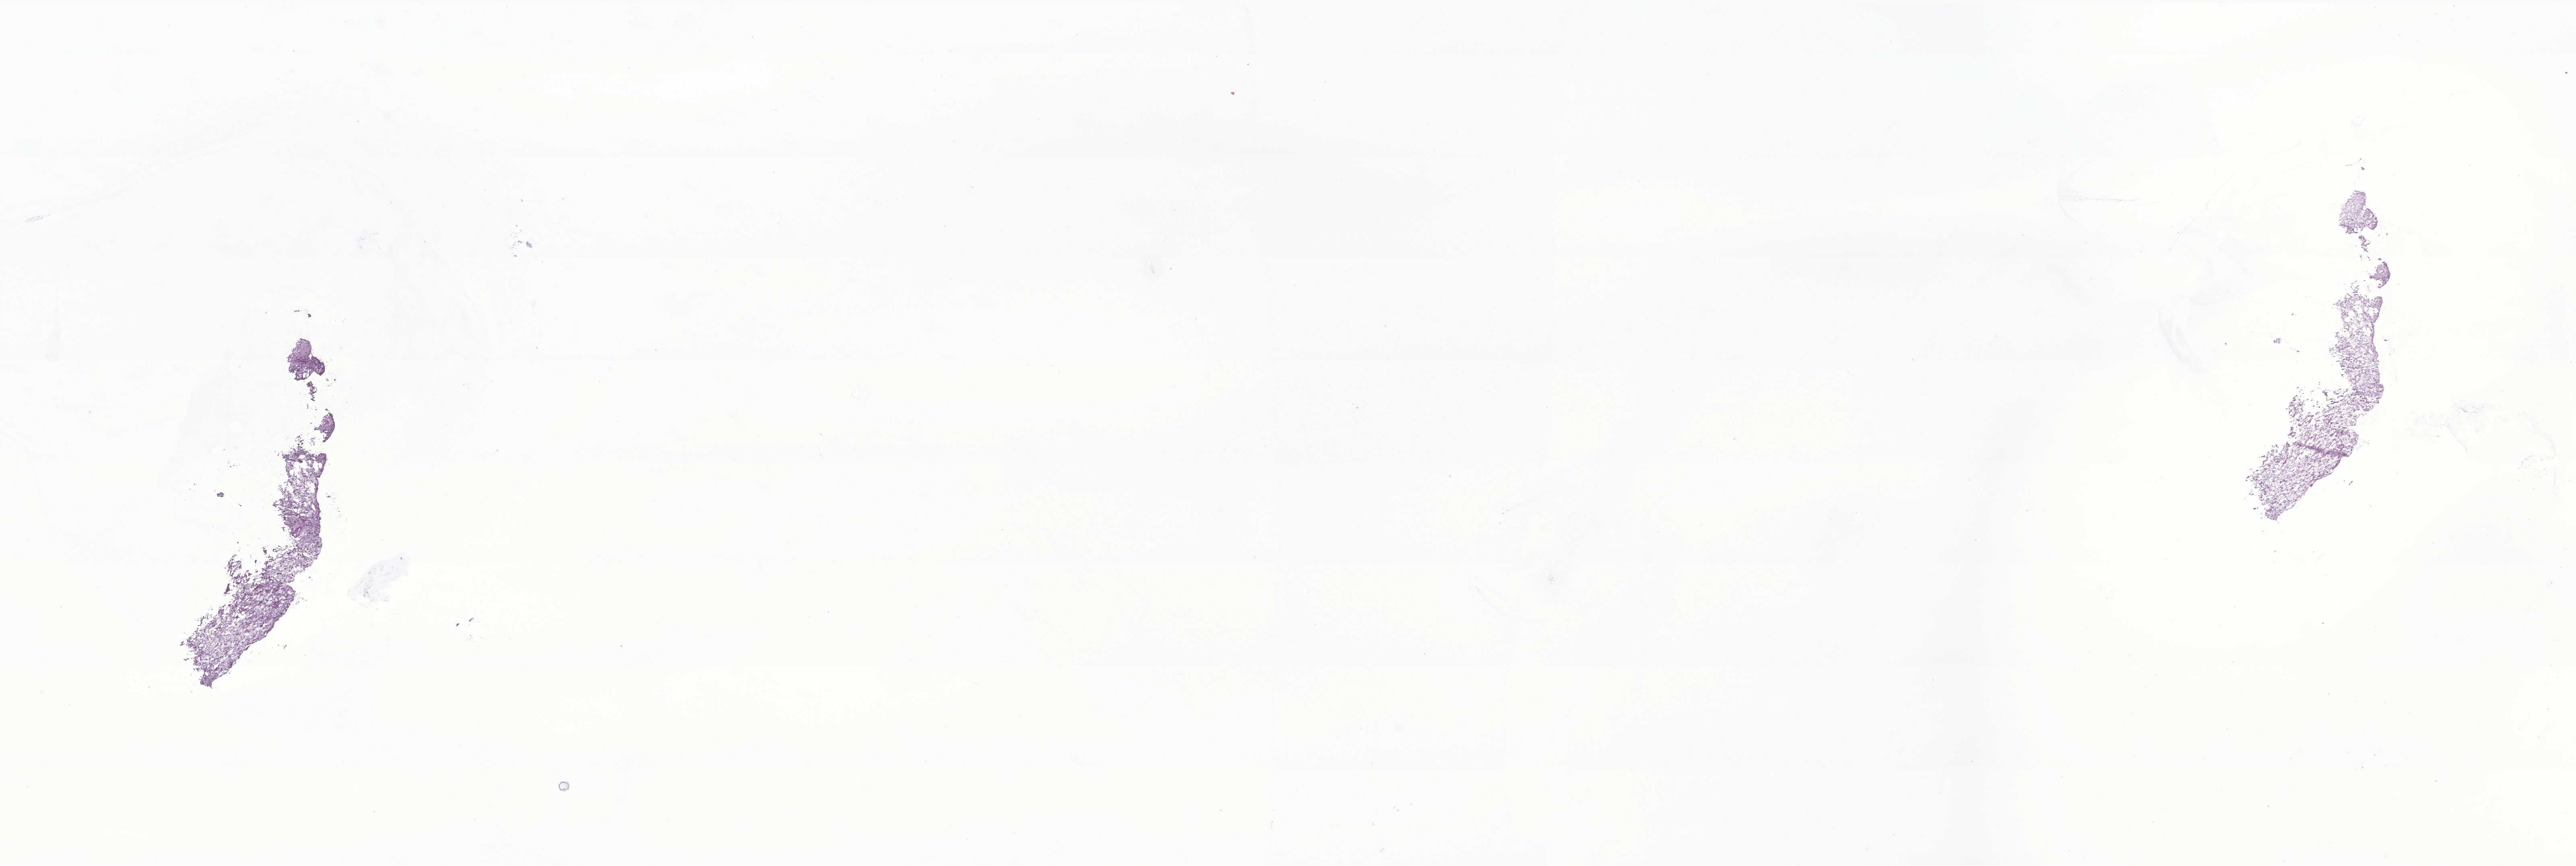
H&E whole-slide image of tumor tissue from the urinary bladder, a low-resolution overview of the entire scanned area, about 27.0 x 9.1 mm. Cryosection (OCT / tissue freezing medium). Patient: male, age 586 days (about 1.6 years).
- recorded diagnosis: Embryonal rhabdomyosarcoma, NOS